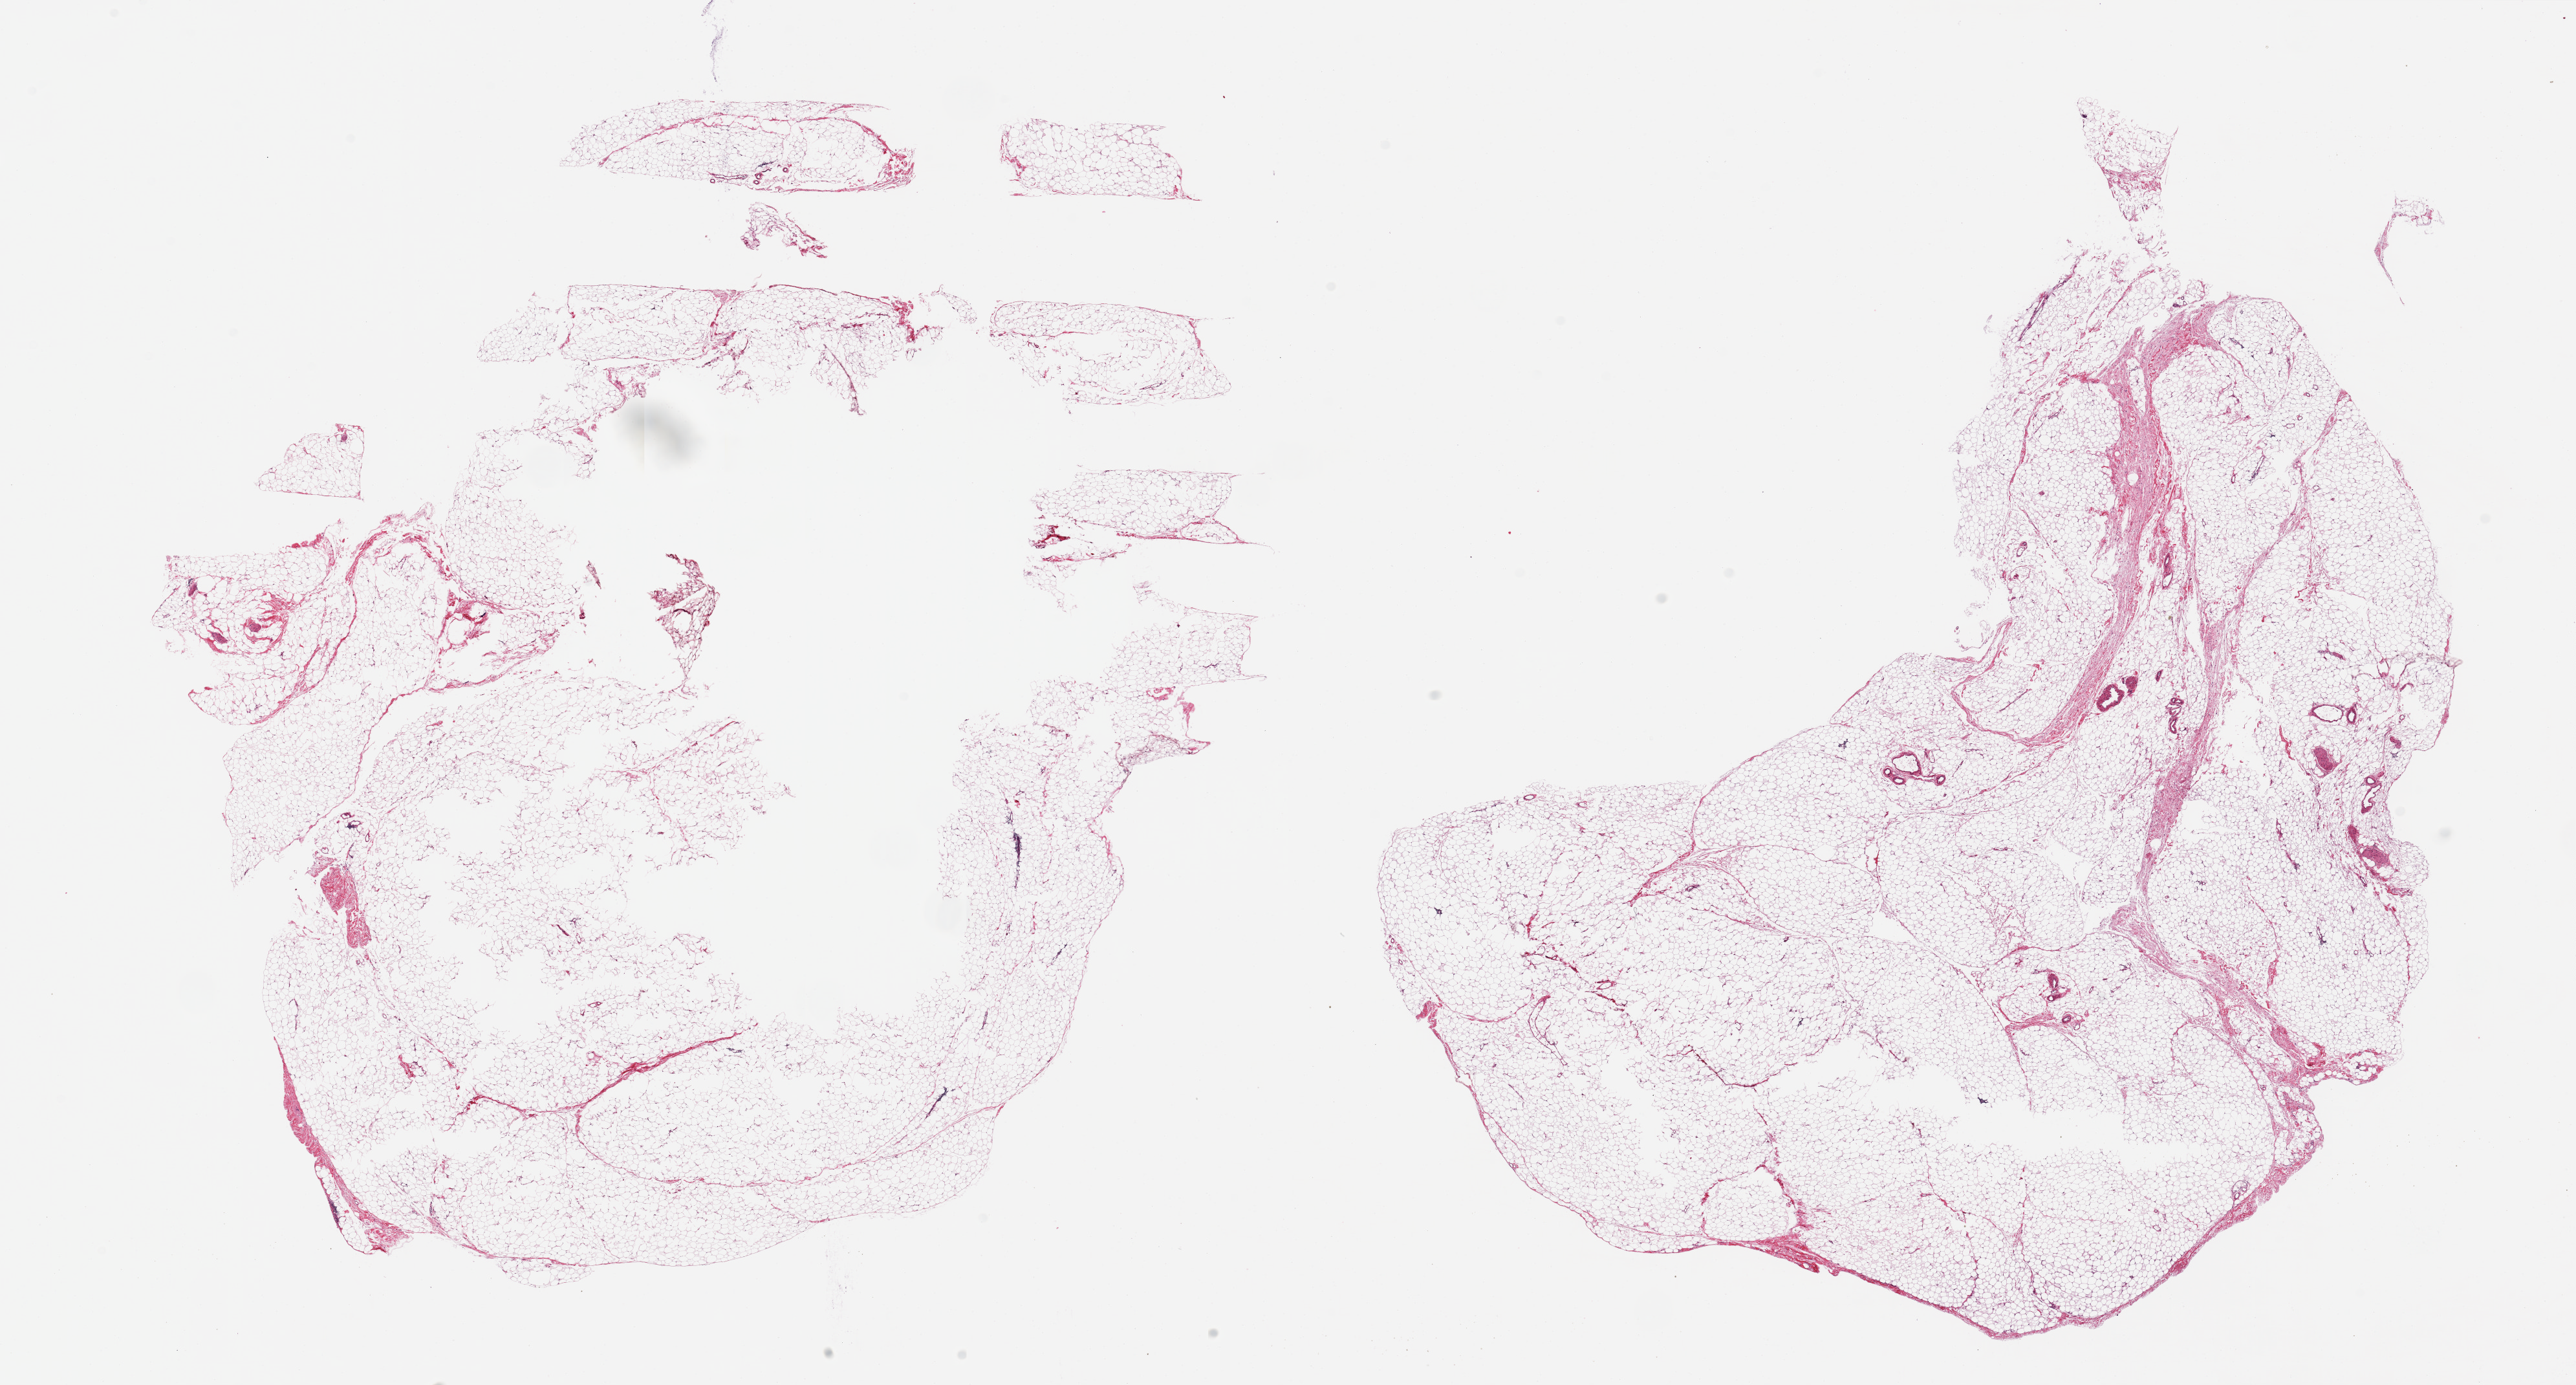
H&E whole-slide image, whole scanned area (about 31.5 x 16.9 mm) shown as a low-resolution overview; PAXgene-fixed paraffin-embedded (PFPE) section; section of omentum (target tissue); tissue donor sample. Male donor.
- pathologist's review note for this sample: 2 pieces, 14x14 & 15x13mm